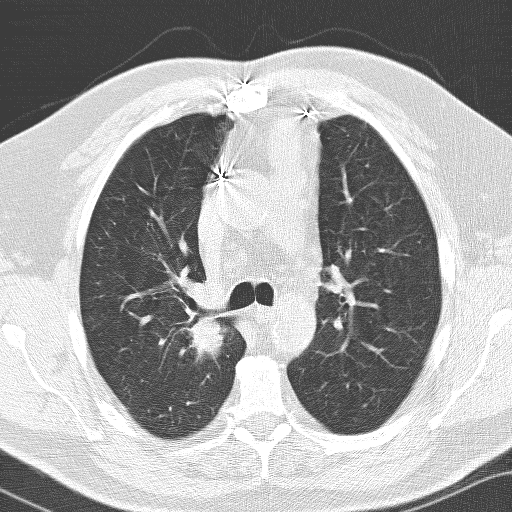
Low-dose screening chest CT, axial slice, baseline annual screen, lung window (W 1500 / L -600 HU), 512 × 512 image matrix. Male participant, aged 66 years at enrolment. Former smoker at enrolment.
Expert reader's lesion annotation, bounding box (x1, y1, x2, y2) in pixels: (145, 293, 232, 390). The exam's reader record, not a measurement of the box and not confirmed to be the same lesion: non-calcified nodule or mass ≥4 mm, right upper lobe, 36 × 30 mm, spiculated (stellate) margins, soft tissue attenuation. Lung cancer was diagnosed 103 days after this screen: adenocarcinoma, NOS, right upper lobe, poorly differentiated (G3), stage IIB (AJCC 6th edition), 33 mm at pathology.